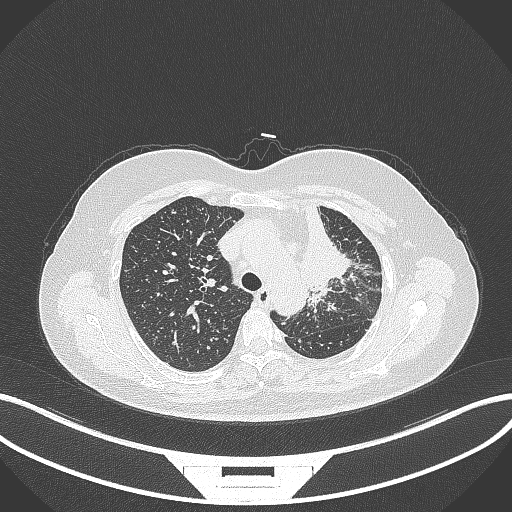
Chest CT, one axial slice. Position 246 of 348 along the scan axis. Reconstruction kernel B70f. 120 kVp. Lung window (W 1500 / L -600 HU). 1 mm slice thickness. 512 × 512 image matrix. Patient: female, 49 years. Case-level facts recorded for this patient, not image findings: clinical TNM (as recorded): T1c N0 M1.
Annotated regions visible in this slice (bounding box drawn by a radiologist):
- lung tumour (recorded histology: adenocarcinoma): box from (x=290, y=196) to (x=352, y=292) px